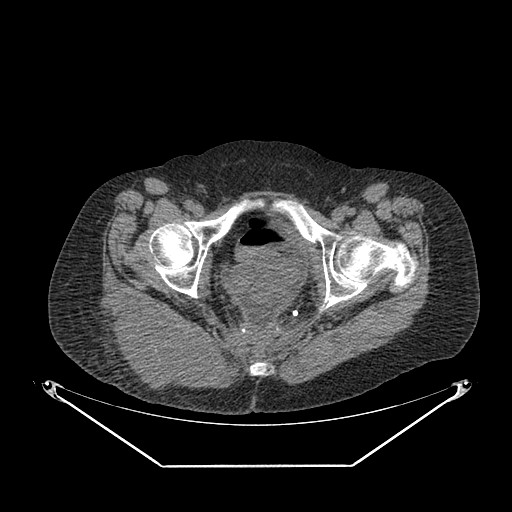
CT of an extremity soft-tissue mass (from a PET/CT study), one axial slice. Position 53 of 267 along the scan axis. 140 kVp. Soft-tissue window (W 400 / L 40 HU). 3.75 mm slice thickness. 512 × 512 image matrix. Female patient. Case-level facts recorded for this patient, not image findings: histological type: spindle cell suggestive of myxofibrosarcoma; grade: intermediate; site of the primary tumour: right buttock.
Structures marked on this image (expert contour drawn on MRI and transferred to this co-registered scan by the dataset authors):
- gross tumour volume (mass): bounding box <107,299,213,394> (left, top, right, bottom; pixels)